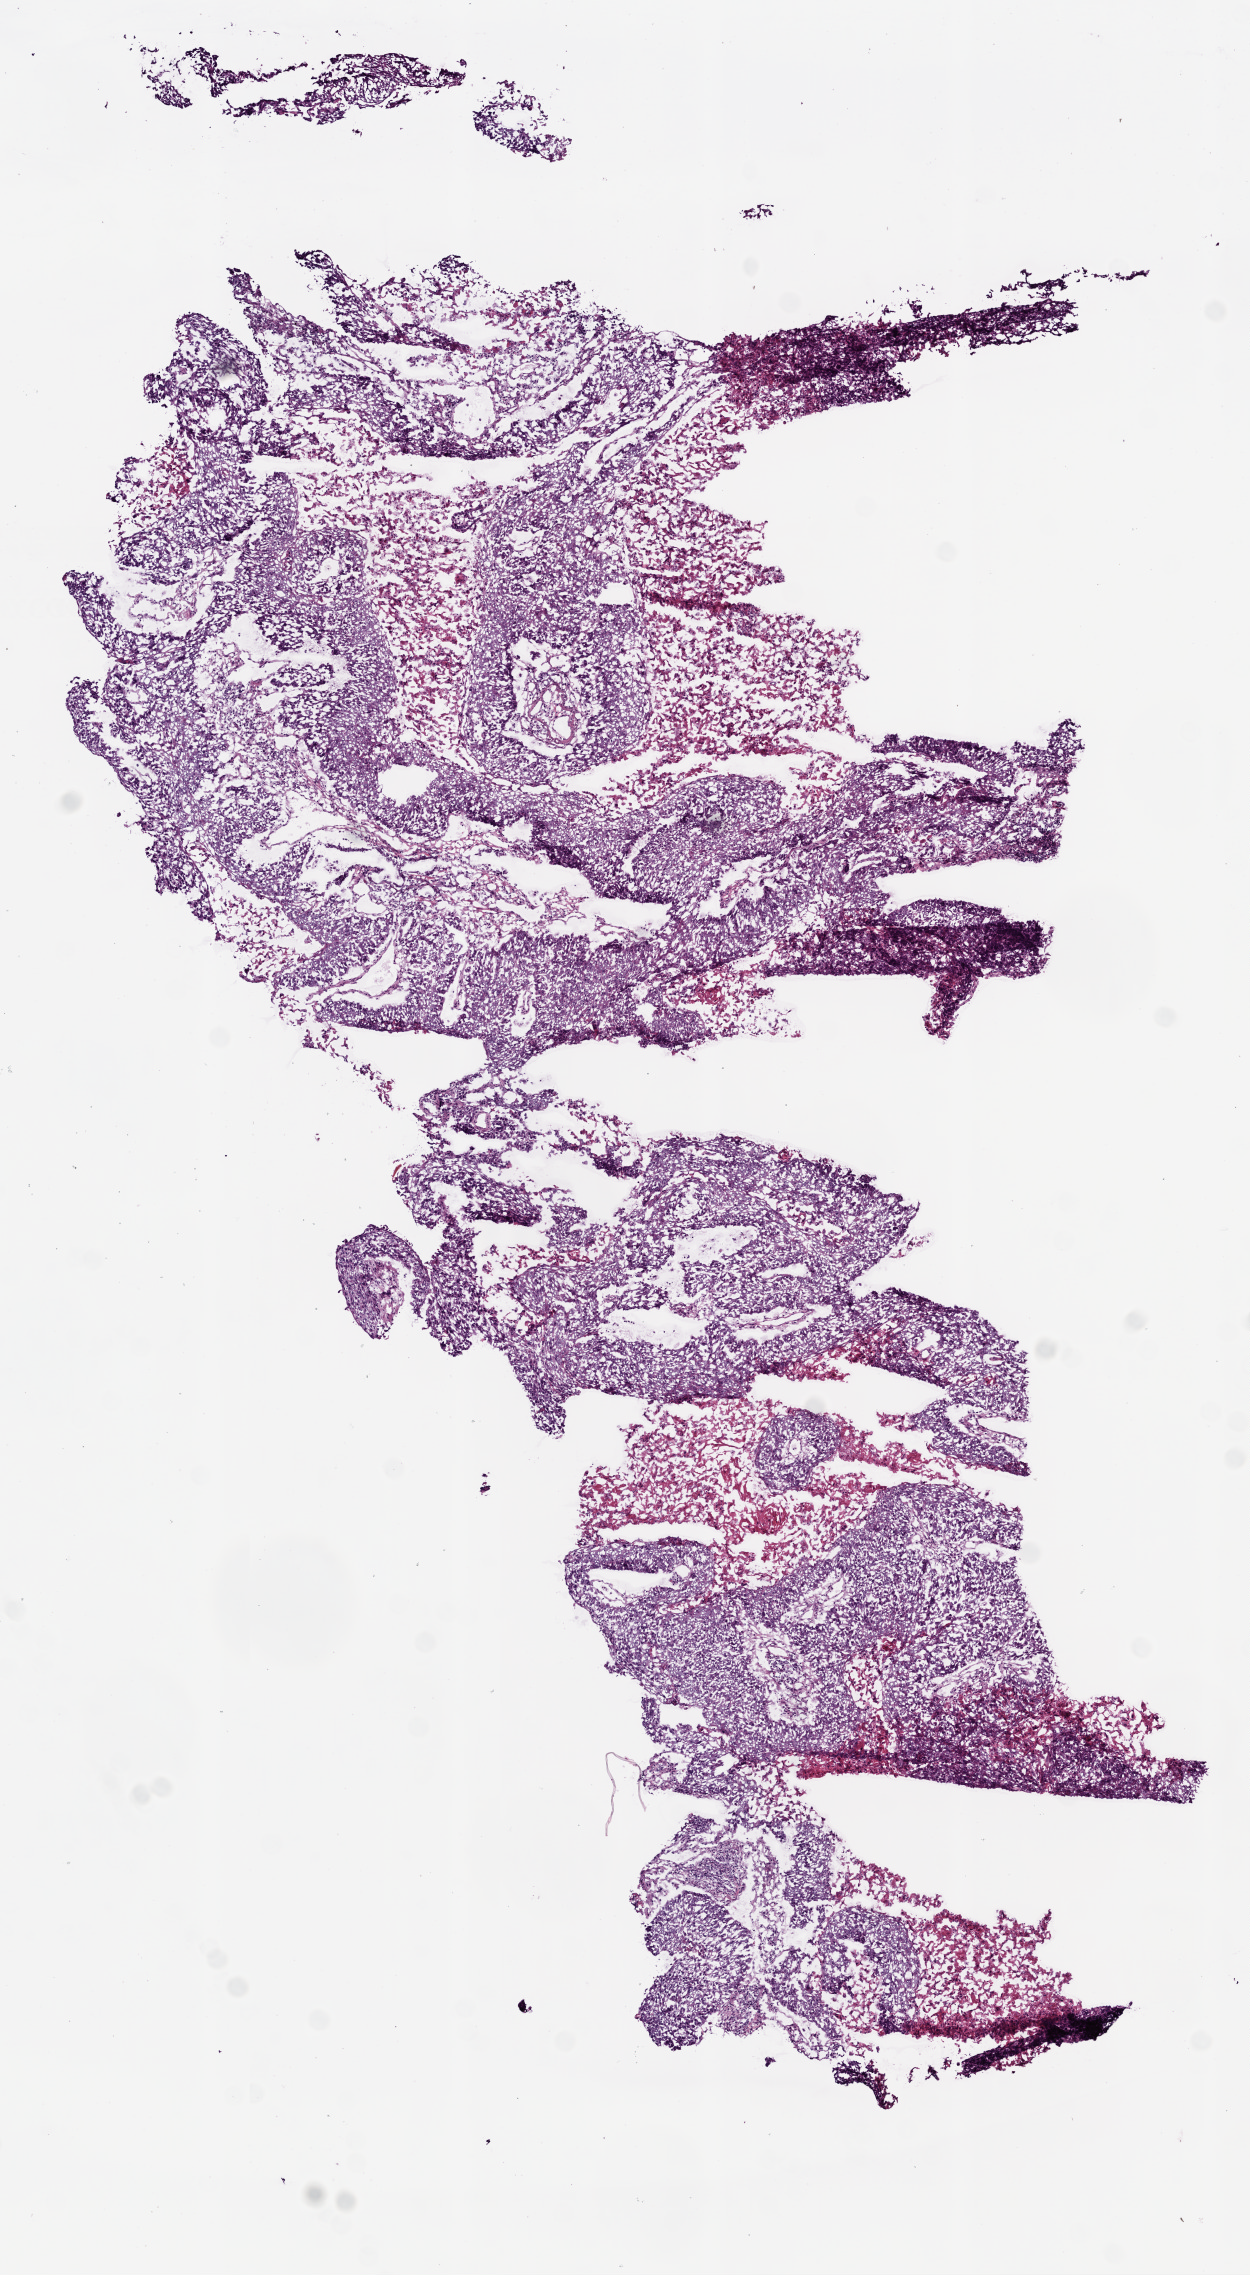
Whole-slide histology image, Hematoxylin and eosin (H&E) stained — whole scanned area (about 5.0 x 9.1 mm) shown as a low-resolution overview; frozen section; primary tumour sample from the lung. Male patient; age at initial diagnosis 73 years. Slide review estimates, as recorded: tumour cells 75%, tumour nuclei 80%, normal cells 0%, stromal cells 10%, necrosis 15%.
• diagnosis: Squamous cell carcinoma, NOS (lower lobe, lung)
• AJCC pathologic stage: IA (5th edition)